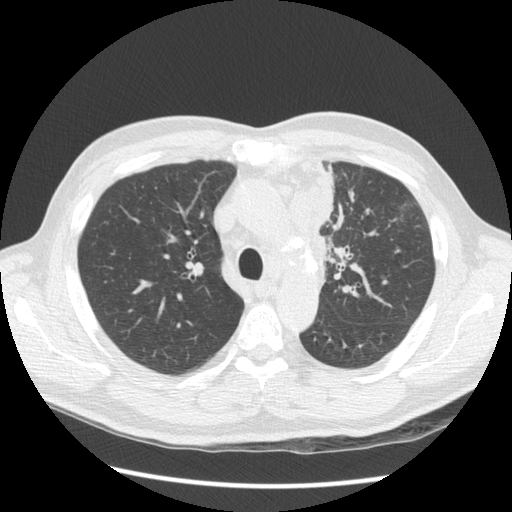
Low-dose screening chest CT, one axial slice. Slice 99 of 136 in the series (ordered by position). 120 kVp. Lung window (W 1500 / L -600 HU). 512 × 512 image matrix.
Outlined on this slice (expert manual segmentation):
- lesion 1 (tumor, upper lobe of left lung): bounding box <292,174,333,284> (left, top, right, bottom; pixels)